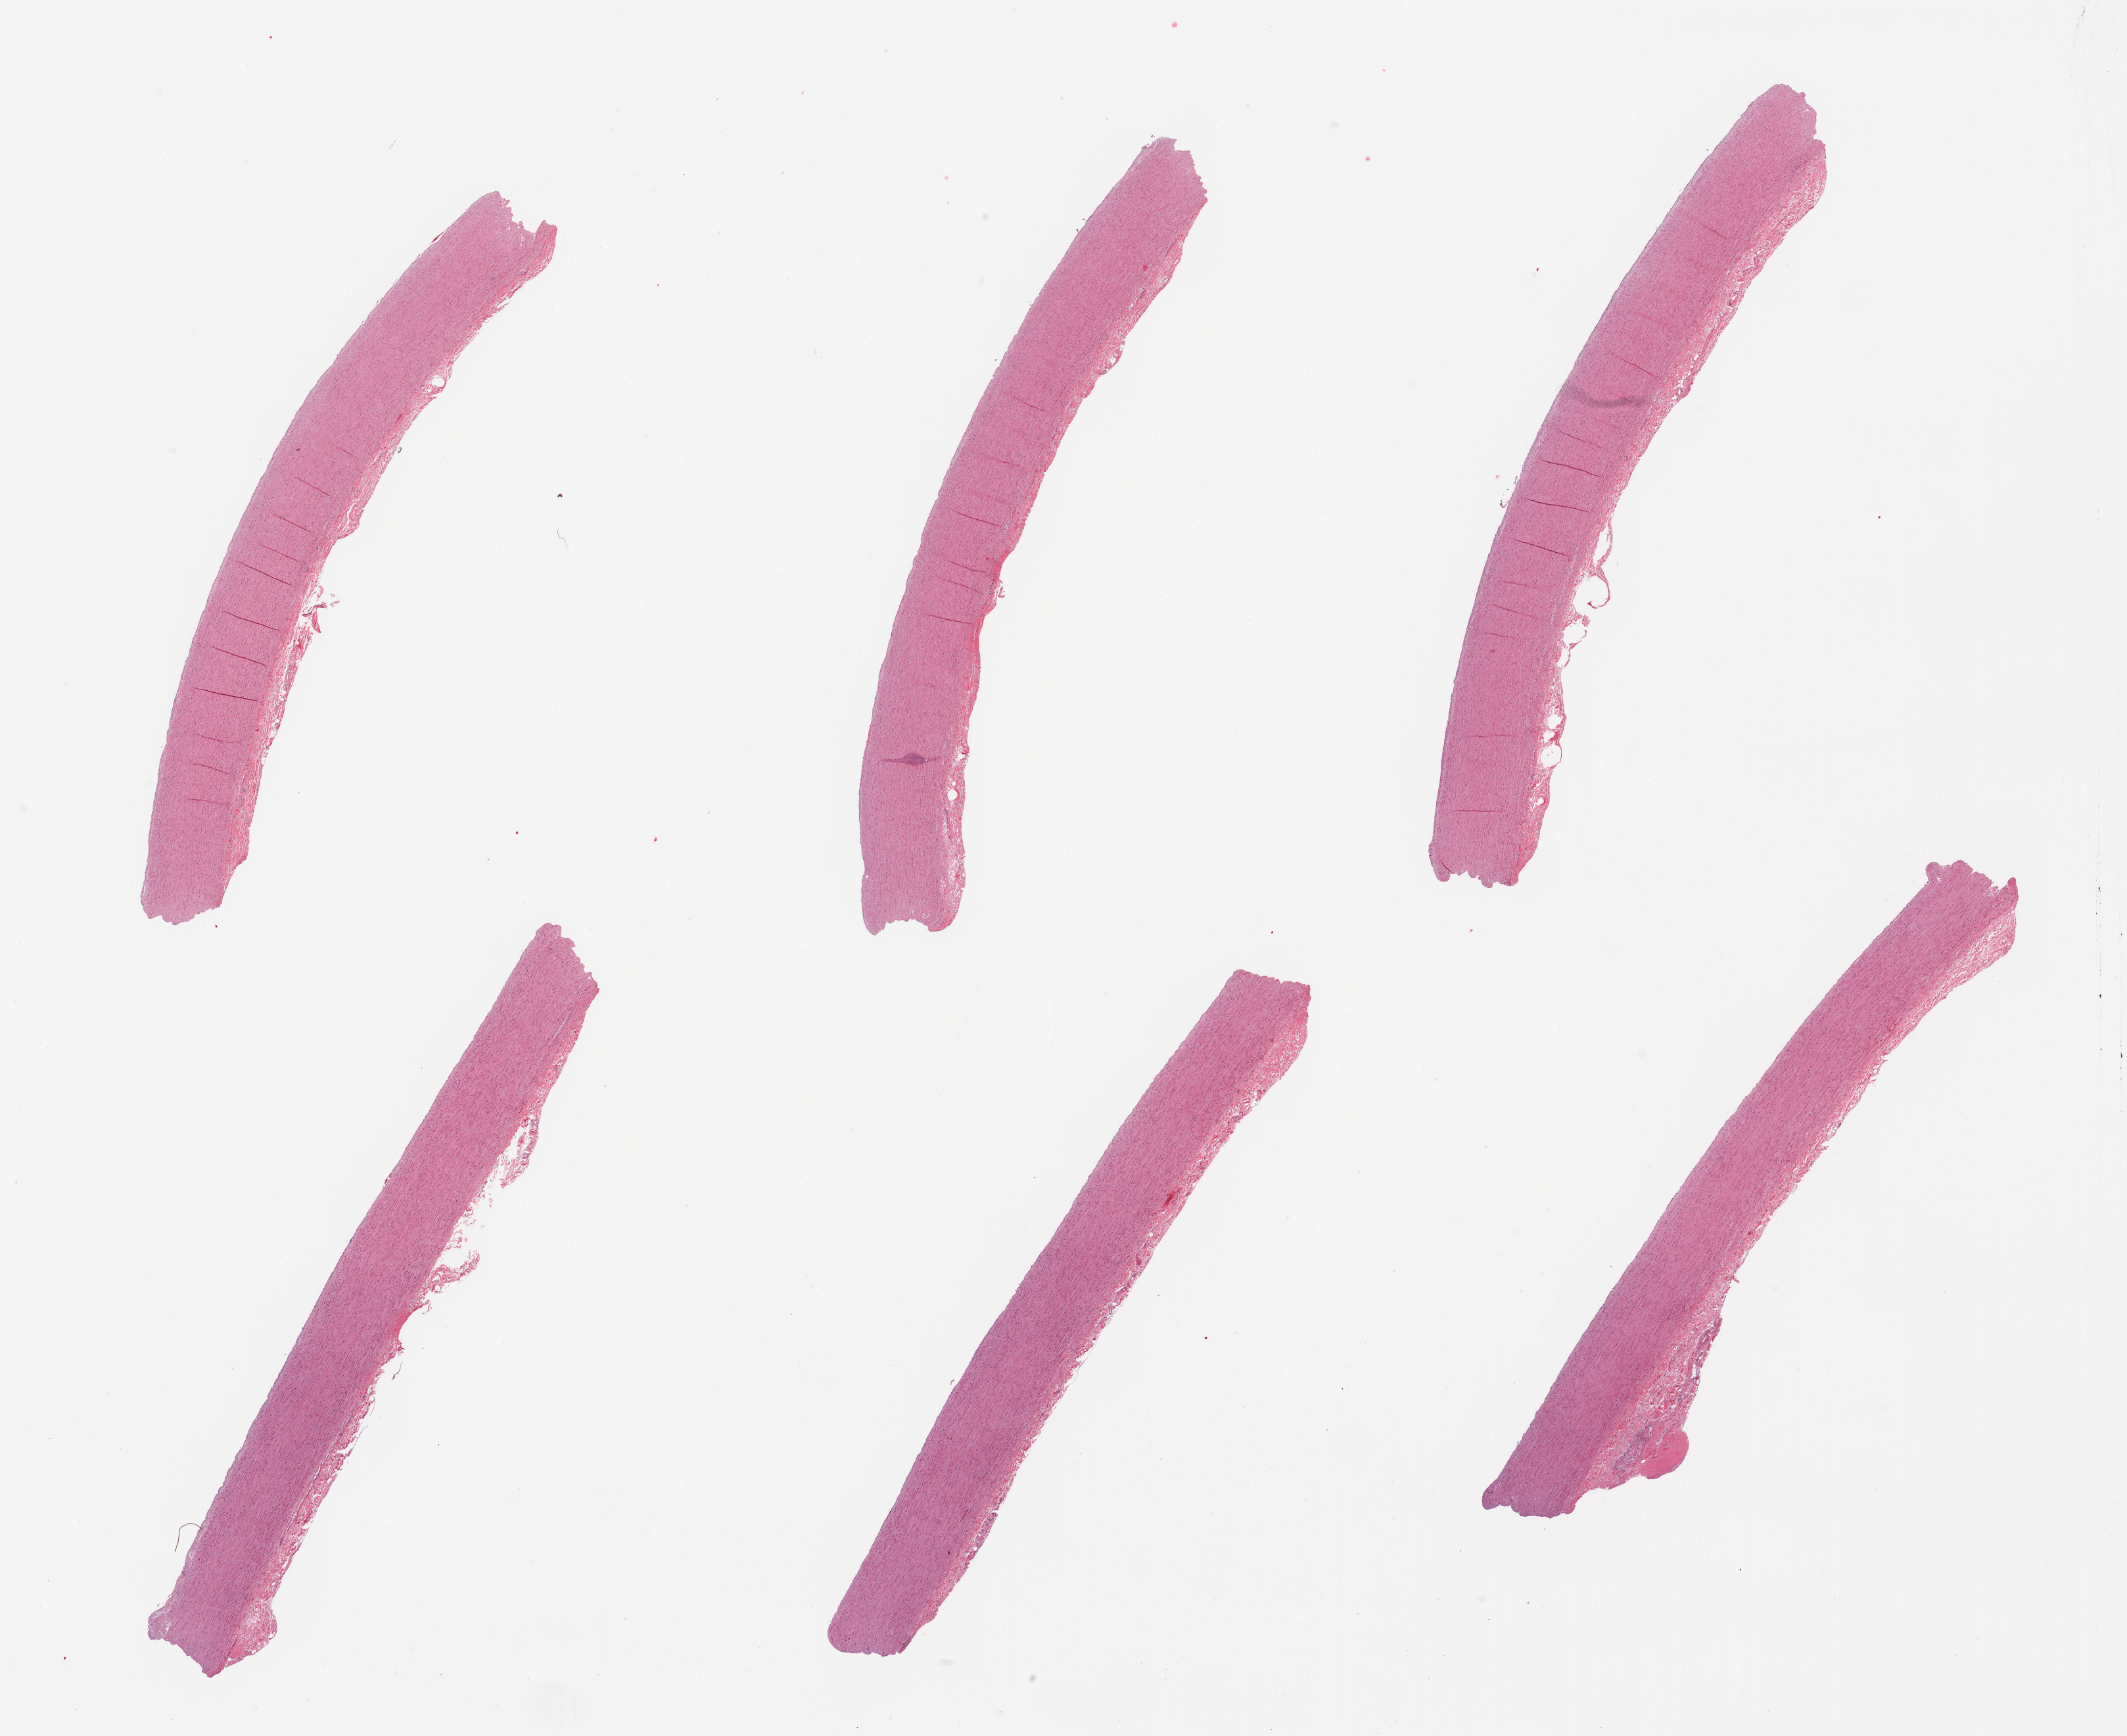
Digitized H&E-stained section — whole scanned area (about 25.6 x 20.9 mm) shown as a low-resolution overview, PAXgene-fixed paraffin-embedded (PFPE) section, target tissue: aorta, donor tissue sample. Donor sex: male.
- pathologist's review note for this sample: 6 pieces, minimal atherosis